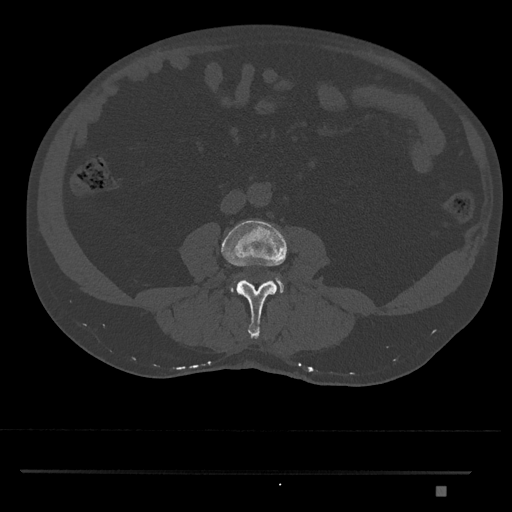
CT including the spine, one axial slice. Reconstruction kernel Br40s/3. 120 kVp. Bone window (W 1800 / L 400 HU). 0.5 mm slice thickness. 512 × 512 image matrix, field of view 429 × 429 mm. Patient: male, 65 years. Case-level facts recorded for this patient, not image findings: primary cancer: prostate.
Structures marked on this image (semi-automatically segmented with operator editing):
- L3 vertebra: bounding box [x1, y1, x2, y2] px = [221, 220, 288, 339]
- L4 vertebra: [231, 275, 284, 293]